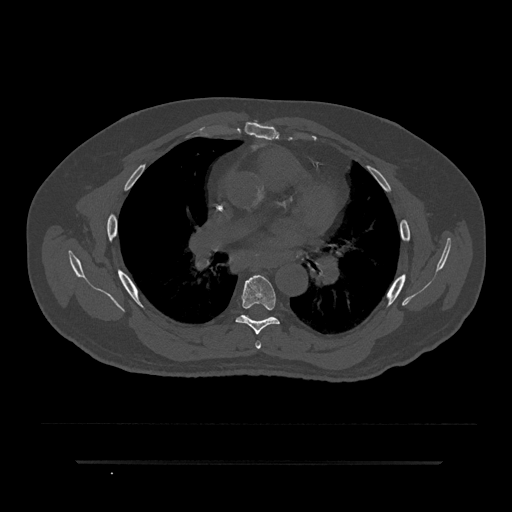
CT including the spine, one axial slice. Slice 526 of 797 in the series (ordered by position). Reconstruction kernel Br40s/3. Bone window (W 1800 / L 400 HU). 512 × 512 image matrix, field of view 464 × 464 mm. Male patient, age 59 years. From the clinical record (not read from this slice): primary cancer: bile ducts; vertebrae with lytic lesions (as recorded): T10.
Annotated regions visible in this slice (semi-automatically segmented with operator editing):
- T5 vertebra: bounding box (x1, y1, x2, y2) in pixels: (255, 341, 261, 349)
- T6 vertebra: (235, 275, 280, 335)